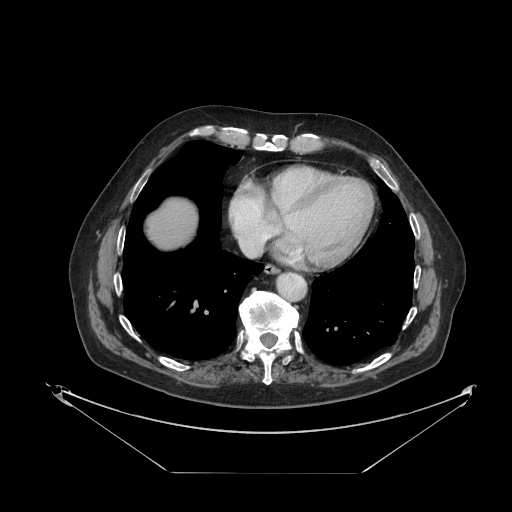
Contrast-enhanced abdominal CT, one axial slice. Slice 121 of 121 in the series (ordered by position). 120 kVp. Intravenous contrast given. Soft-tissue window (W 400 / L 40 HU). 2.5 mm slice thickness. 512 × 512 image matrix, field of view 500 × 500 mm. Male patient, age 68 years. From the clinical record (not read from this slice): diagnosis: colorectal cancer liver metastases, imaged before liver resection; multiple liver metastases: no; largest metastasis: 4 cm.
Annotated regions visible in this slice (manually delineated by an expert):
- liver: box from (x=146, y=199) to (x=197, y=248) px
- planned liver remnant (the part of the liver to remain after resection): (x=146, y=200)–(x=197, y=248)